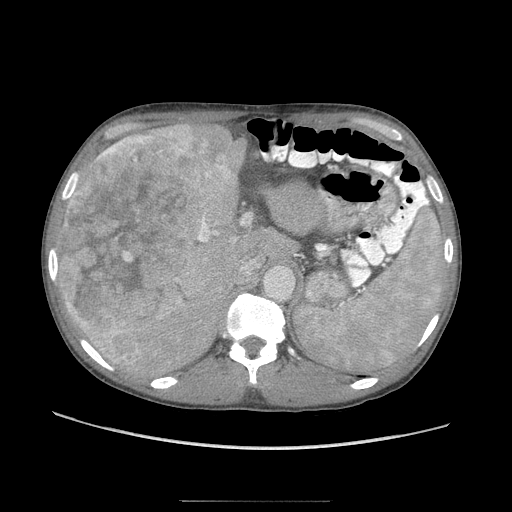
Contrast-enhanced abdominal CT (liver protocol), one axial slice; position 64 of 103 along the scan axis; soft-tissue window (W 400 / L 40 HU); 2.5 mm slice thickness; 512 × 512 image matrix. From the clinical record (not read from this slice): diagnosis: hepatocellular carcinoma (patient treated with transarterial chemoembolisation; whether this scan precedes or follows treatment is not stated here); TNM stage (as recorded): Stage-IIIA; Child-Pugh class: A; tumour nodularity: multinodular.
Structures marked on this image (semi-automatically segmented with operator editing):
- liver parenchyma outside the tumour (the mass and vessels are separate outlines, so this box may not span the whole liver): bounding box [x1, y1, x2, y2] px = [58, 120, 288, 378]
- mass: [54, 120, 234, 364]
- liver vessels: [106, 222, 218, 370]